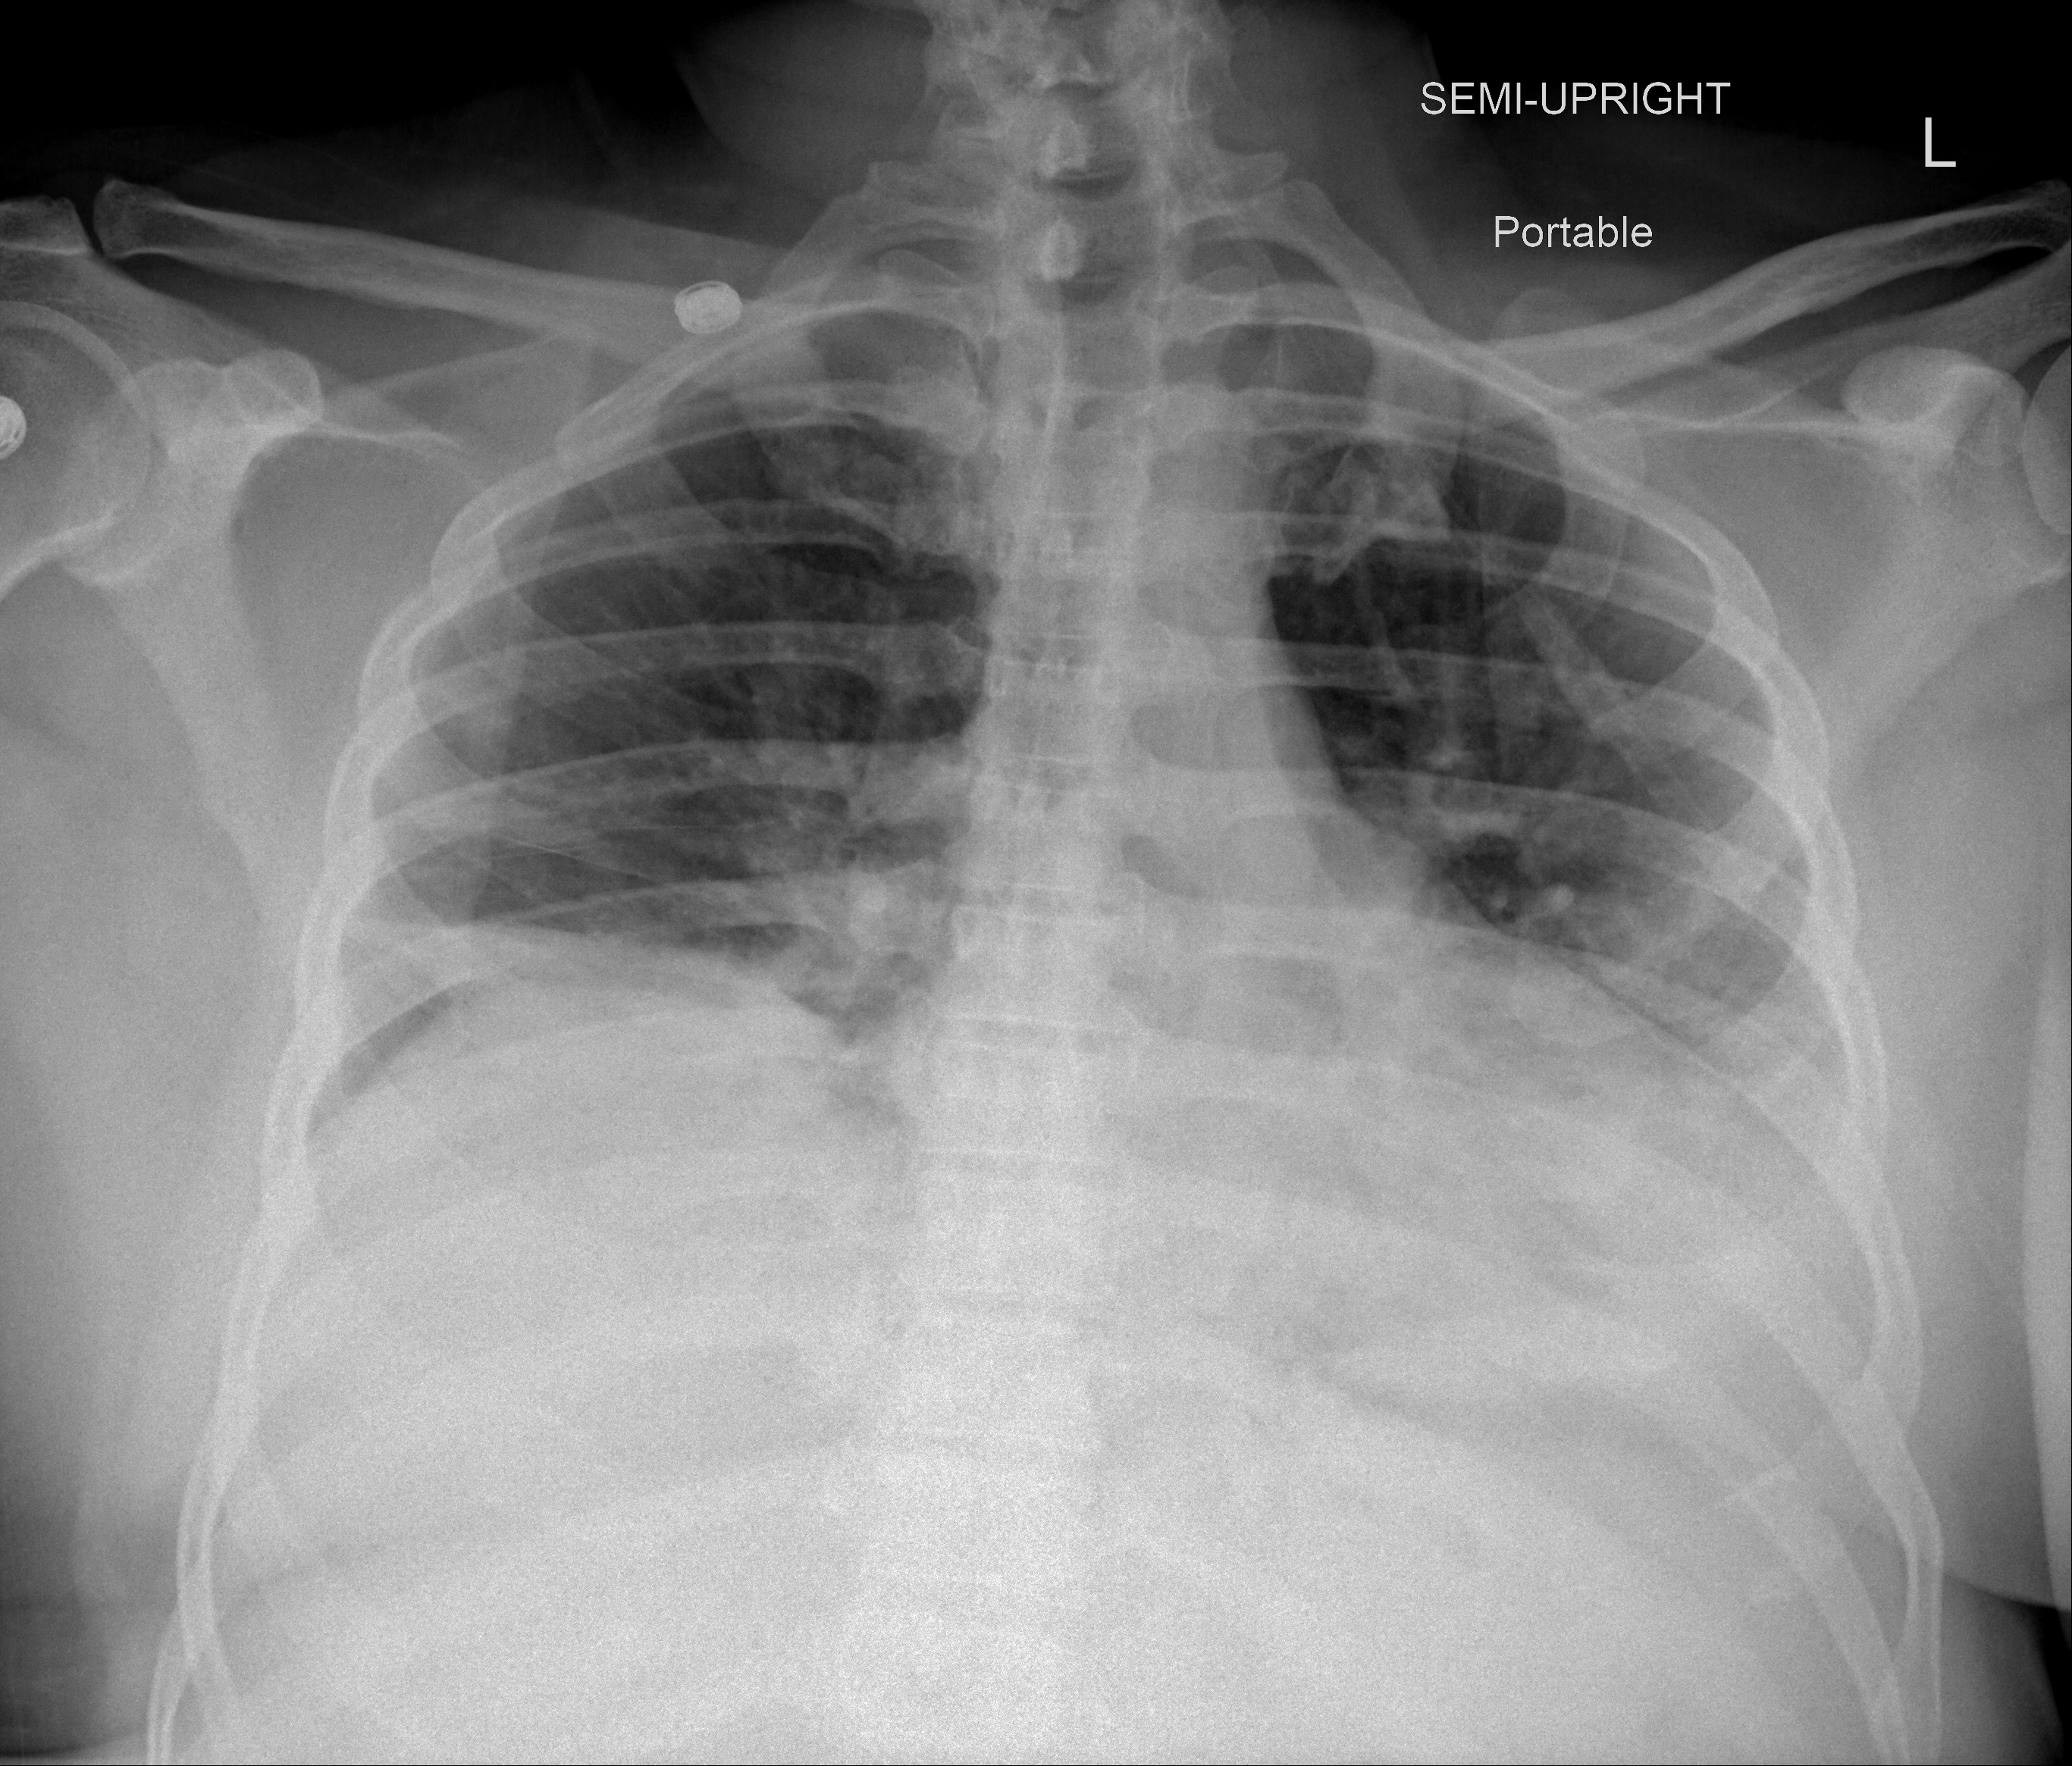
Portable chest radiograph, AP projection. Male patient, age 63 years; COVID-19 (test-positive).
Radiologist's key findings for this exam: blunting of the left costophrenic angle suggestive of small pleural effusion.